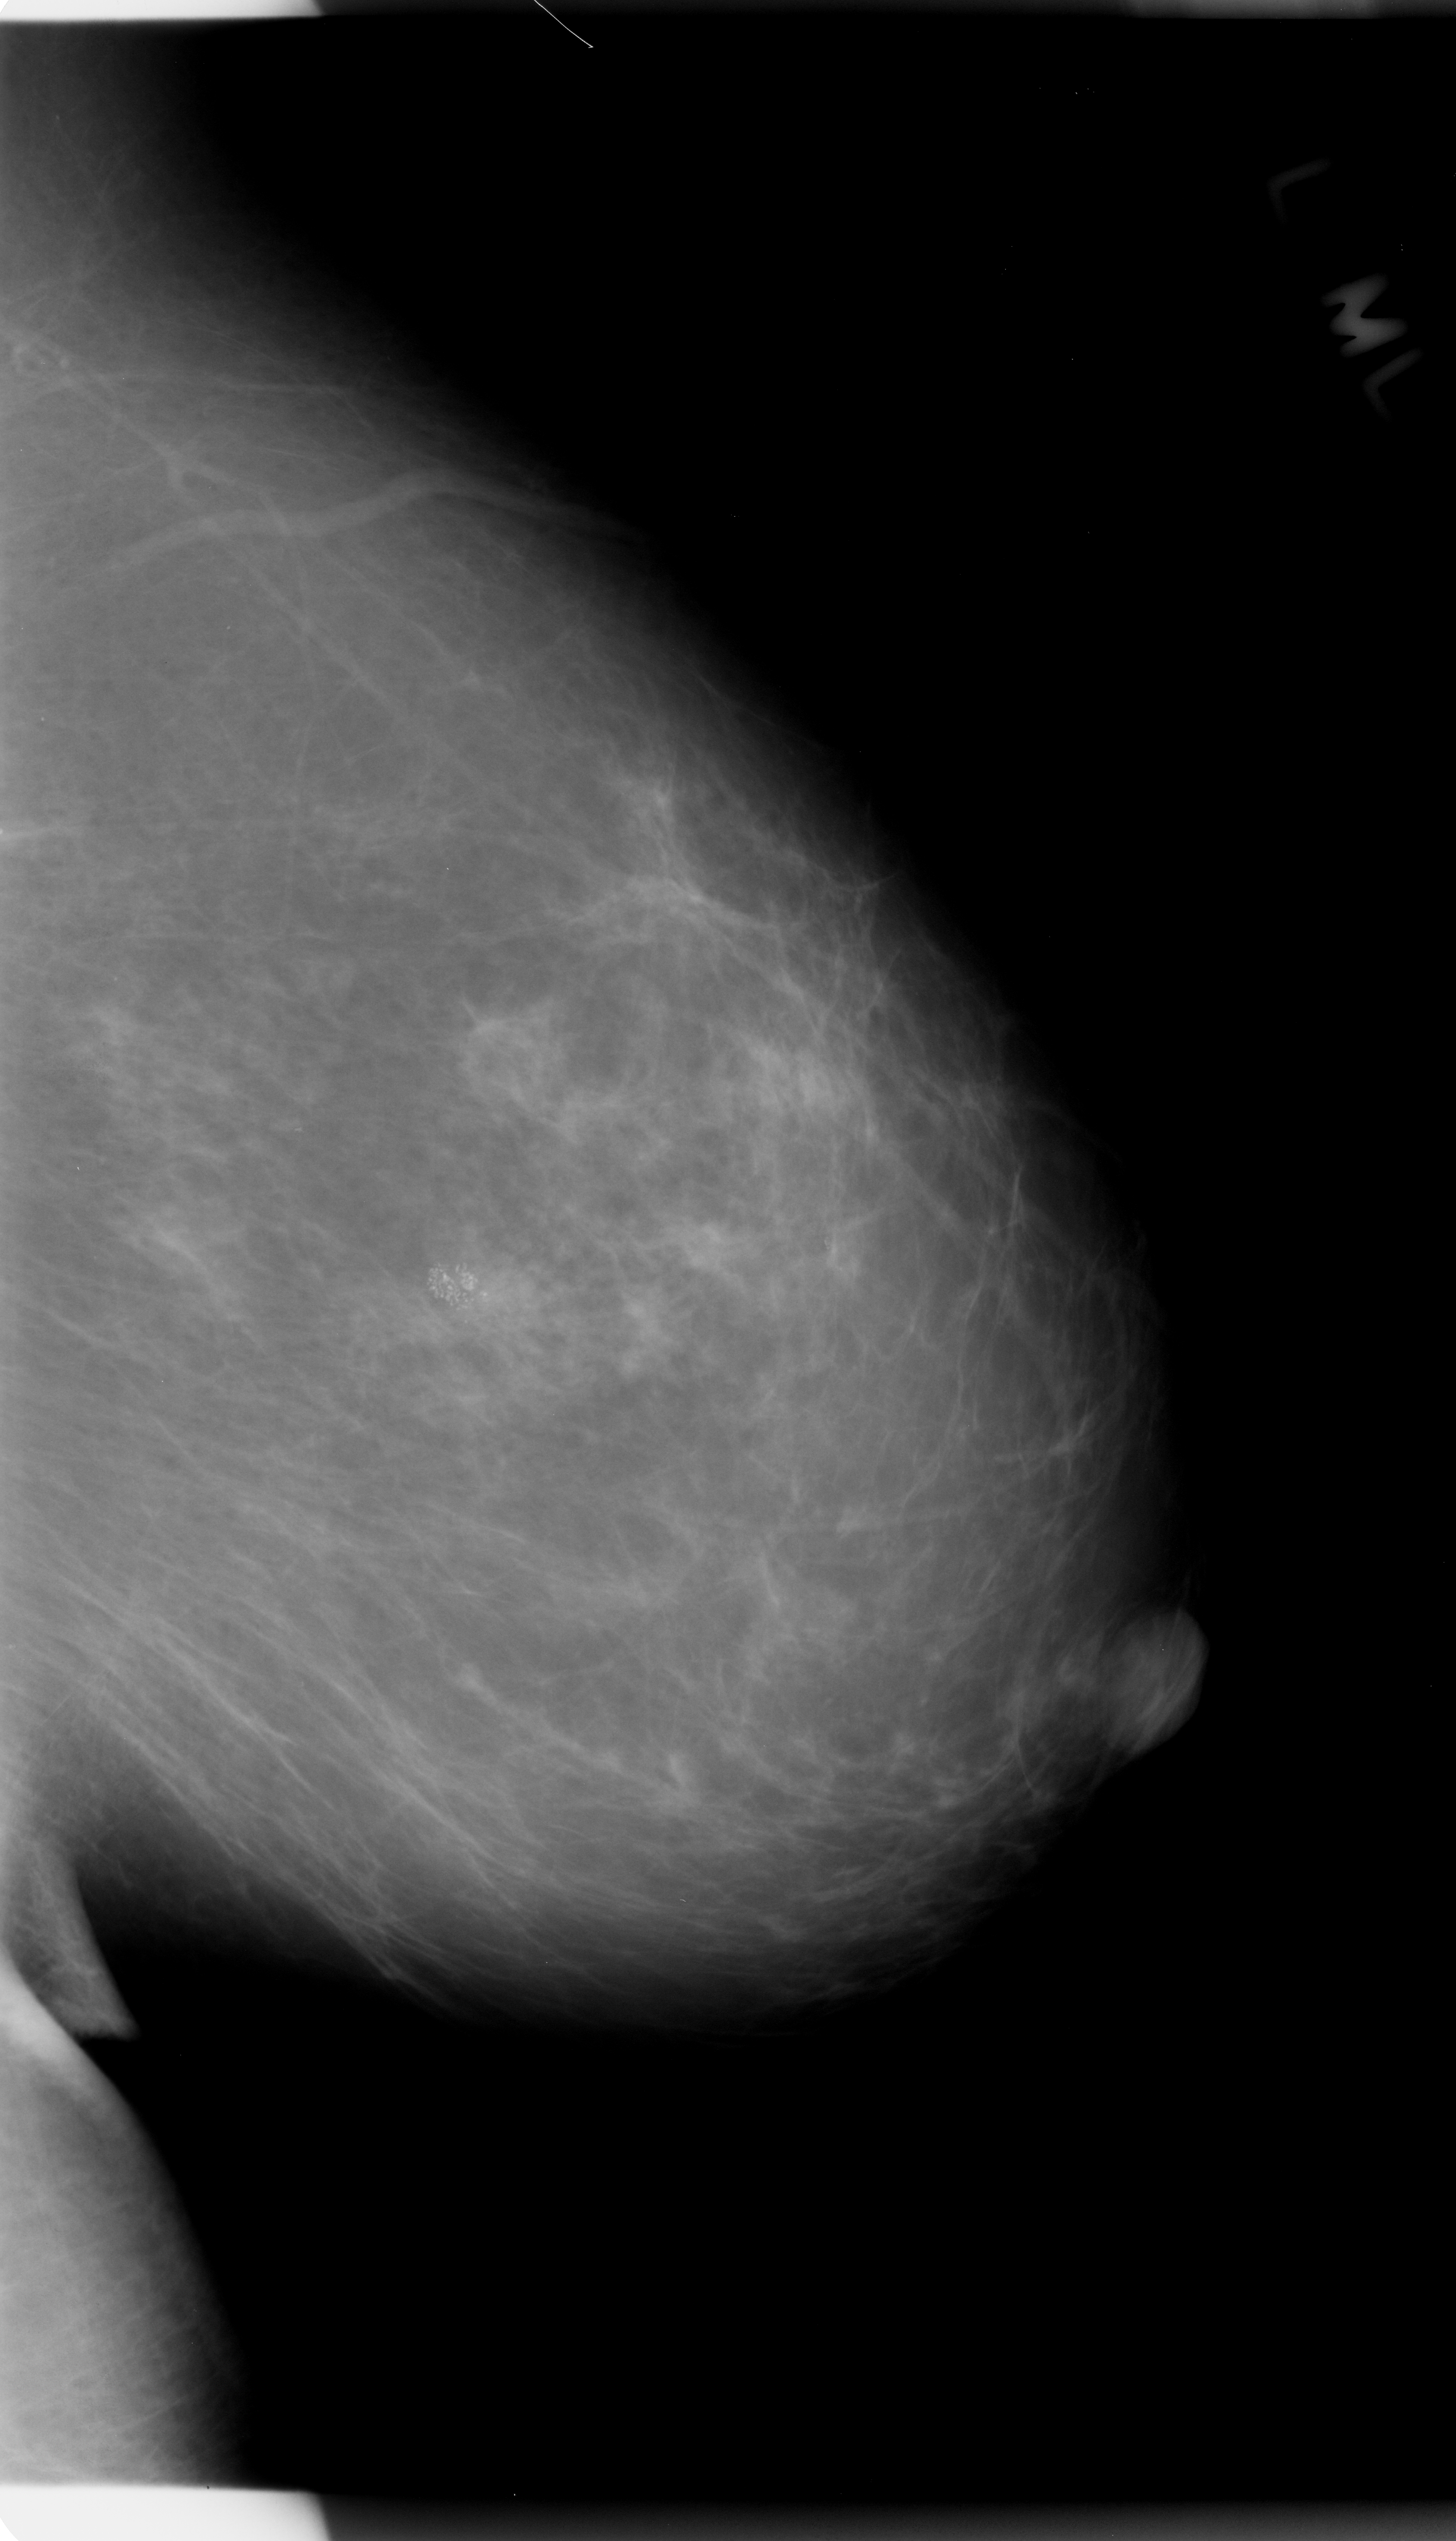
Mammogram (digitized film). Left breast. Mediolateral oblique (MLO) view. 1456 × 2541 image matrix.
Expert-marked regions of interest on this film, with their recorded descriptors:
- calcifications, morphology pleomorphic, distribution clustered; BI-RADS assessment category 4; subtlety rating 5 on a 1 (subtle) to 5 (obvious) scale; pathology (as recorded): malignant: box from (x=364, y=1198) to (x=552, y=1395) px